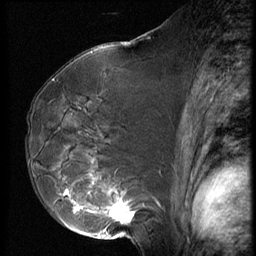
Breast MRI (dynamic contrast-enhanced), one sagittal slice; position 37 of 62 along the scan axis; 3 images stored at this slice position (order not interpretable as contrast timing); 1.5 T; TE 4.2 ms, TR 9 ms; 2.5 mm slice thickness; 256 × 256 image matrix, field of view 180 × 180 mm. Patient: female, 50 years. Case-level facts recorded for this patient, not image findings: setting: breast cancer imaged before/during neoadjuvant chemotherapy; receptor status: HR-positive, HER2-negative.
Structures marked on this image (semi-automatic segmentation, software-assisted and operator-edited):
- analysis volume of interest (the breast-tissue region the enhancement analysis was run in; not a lesion): bounding box <59,125,139,238> (left, top, right, bottom; pixels)
- tumour enhancement mask (voxels above the 140 % enhancement threshold inside the analysis volume of interest): <65,190,135,231>